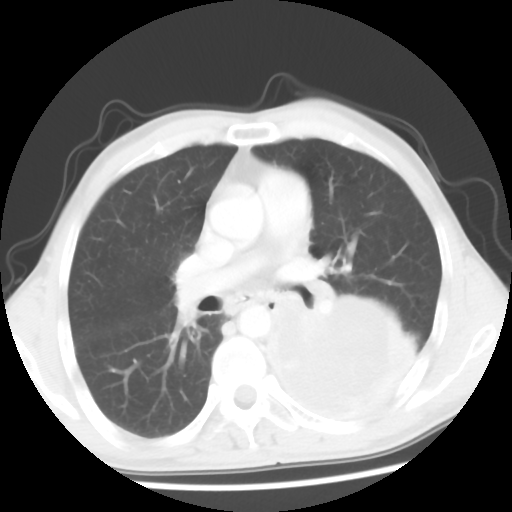
Chest CT, one axial slice. Position 32 of 56 along the scan axis. 120 kVp. Lung window (W 1500 / L -600 HU). 5 mm slice thickness. 512 × 512 image matrix. Male patient, age 60 years. Case-level facts recorded for this patient, not image findings: clinical TNM (as recorded): T4 N0 M0.
Annotated regions visible in this slice (rectangle marked by the reading radiologist):
- lung tumour (recorded histology: squamous cell carcinoma): bounding box <245,274,426,426> (left, top, right, bottom; pixels)